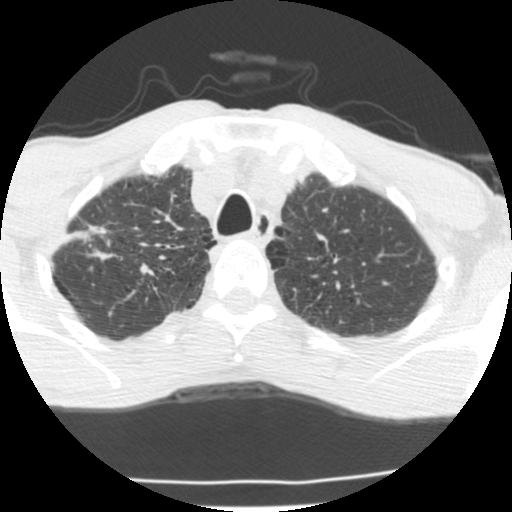
Low-dose screening chest CT, one axial slice; slice 177 of 214 in the series (ordered by position); 120 kVp; lung window (W 1500 / L -600 HU); 2.5 mm slice thickness; 512 × 512 image matrix, field of view 283 × 283 mm.
Annotated regions visible in this slice (manually delineated by an expert):
- lesion 1 (tumor, upper lobe of right lung): bounding box [x1, y1, x2, y2] px = [88, 225, 108, 237]